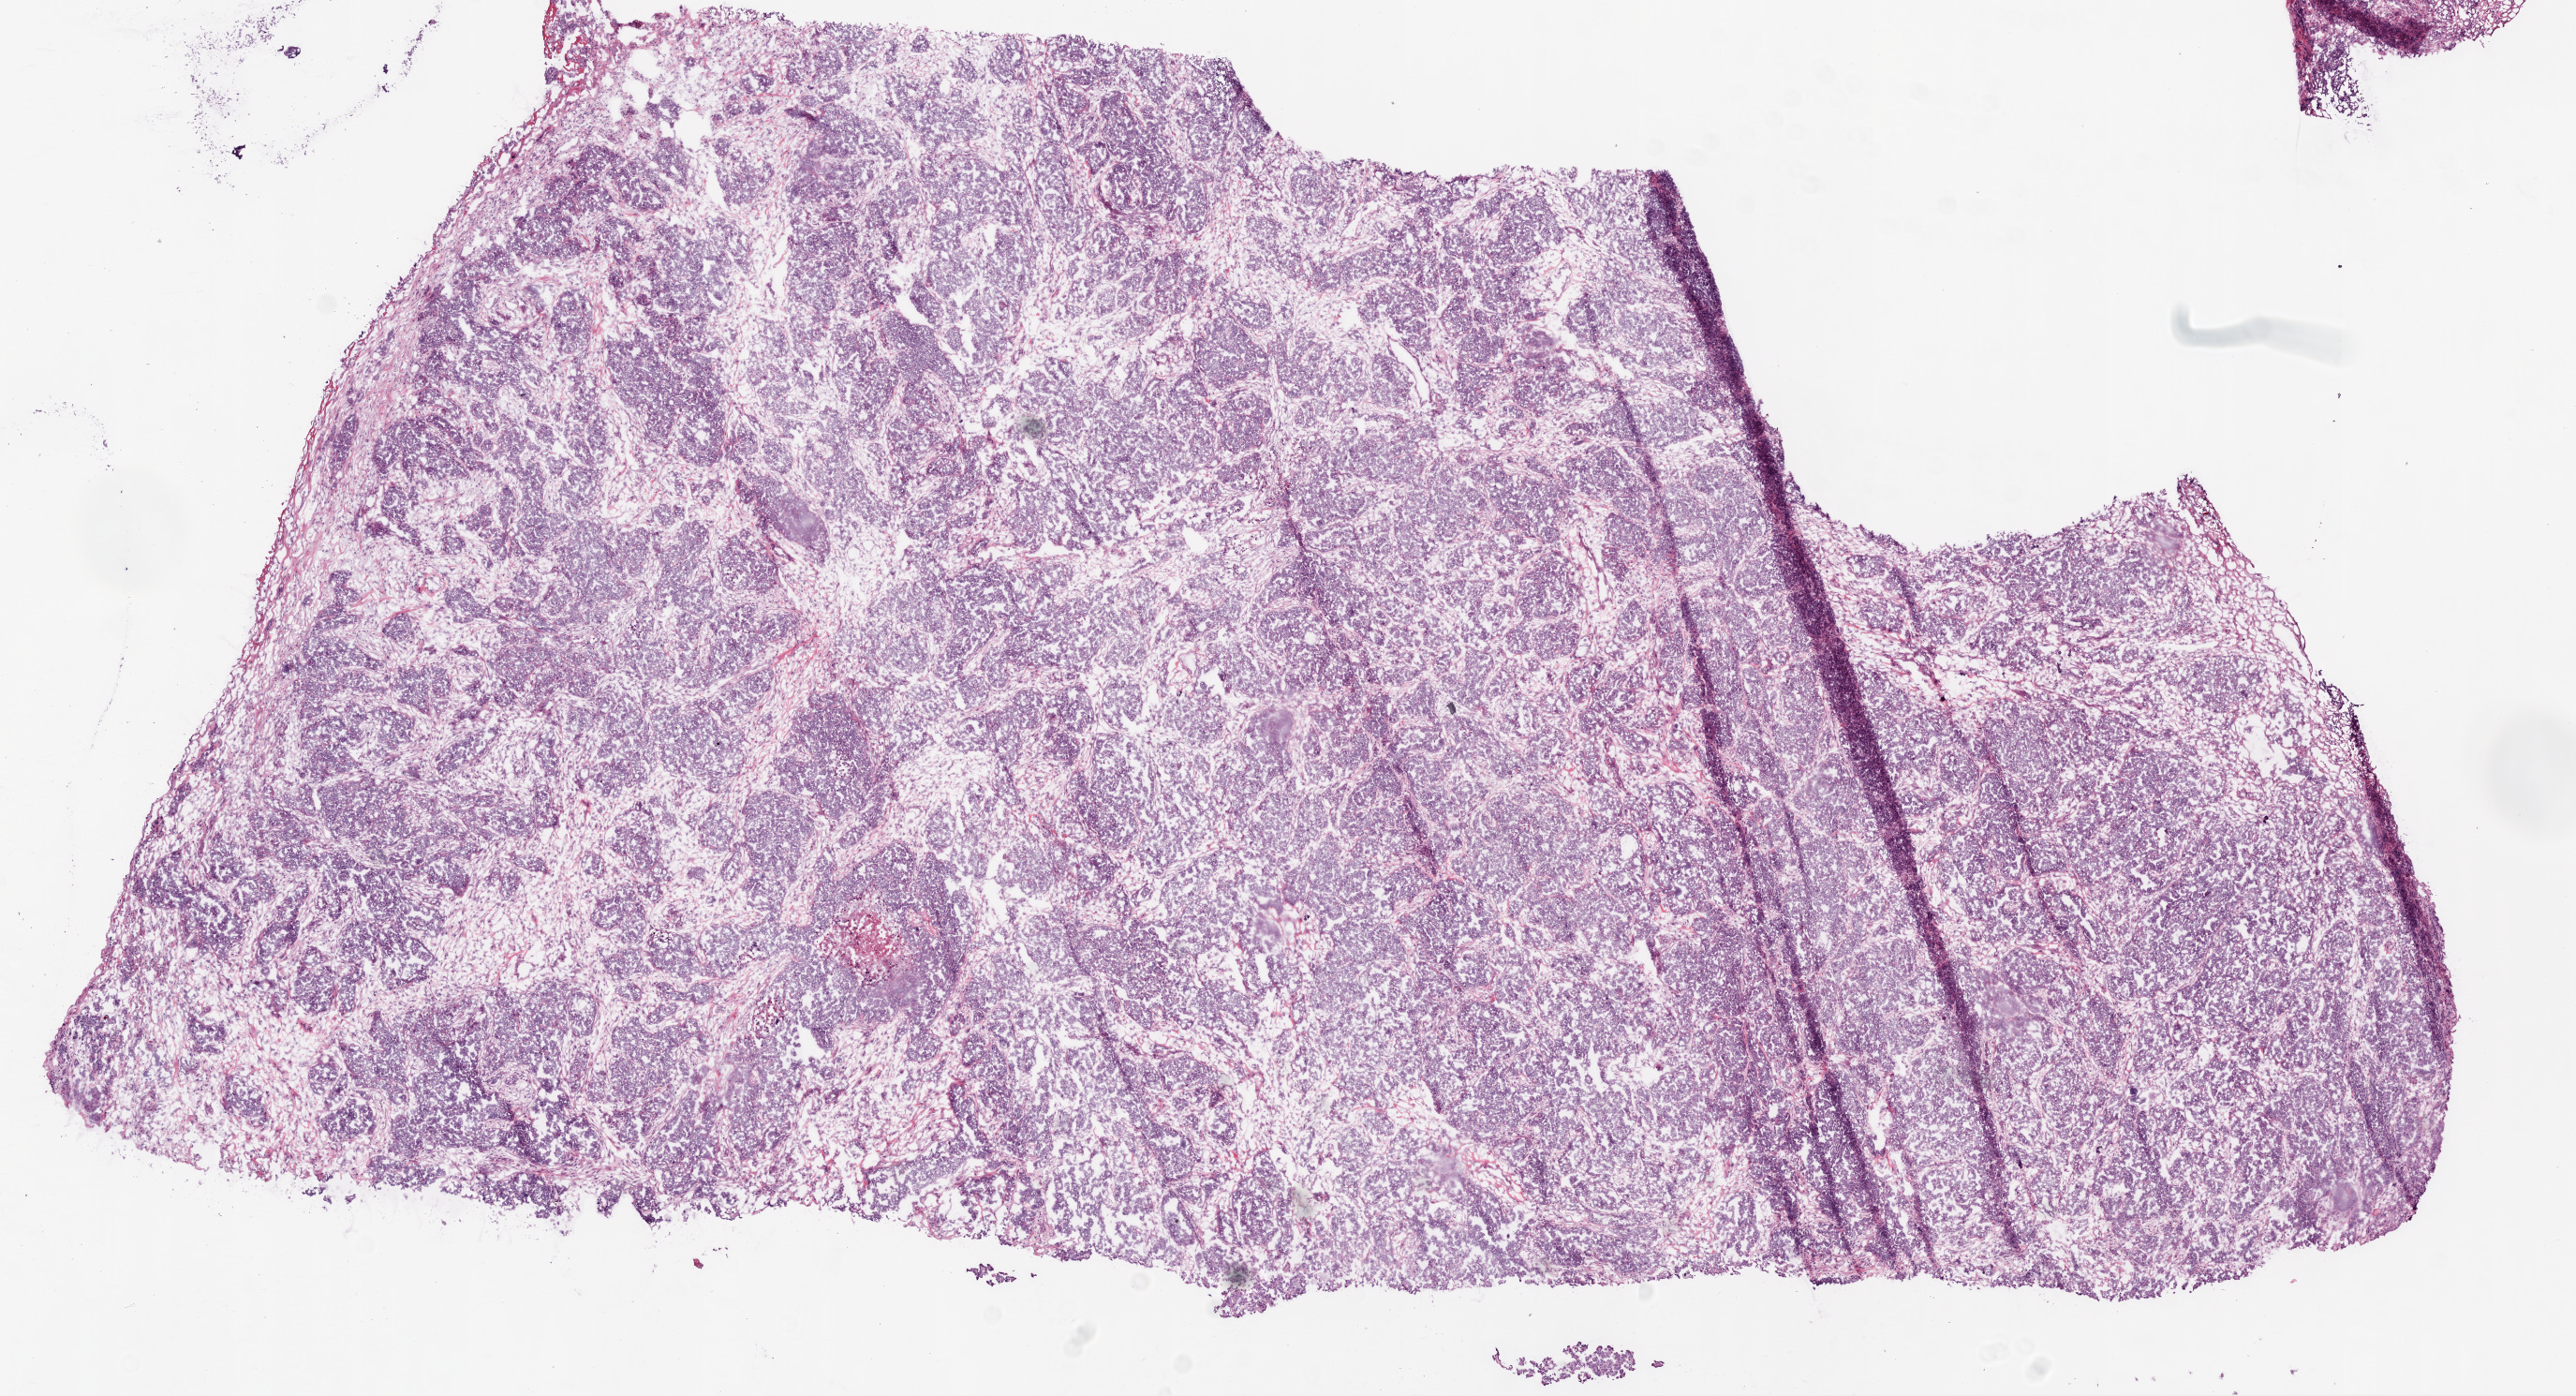
Digitized Hematoxylin and eosin (H&E) stained tissue section (whole slide), a low-resolution overview of the entire scanned area, about 11.0 x 6.0 mm (acquisition: 20x scan); frozen section from the bottom of the tissue portion; primary tumour sample from the ovary. Patient: female, age at initial diagnosis 71 years. Histologic grade: G3 (poorly differentiated). Pathologist review of this section (percent, as recorded): tumour cells 95%, tumour nuclei 85%, normal cells 0%, stromal cells 0%, necrosis 5%.
Laterality: bilateral. Diagnosis: Serous cystadenocarcinoma, NOS. FIGO stage: IIIC.